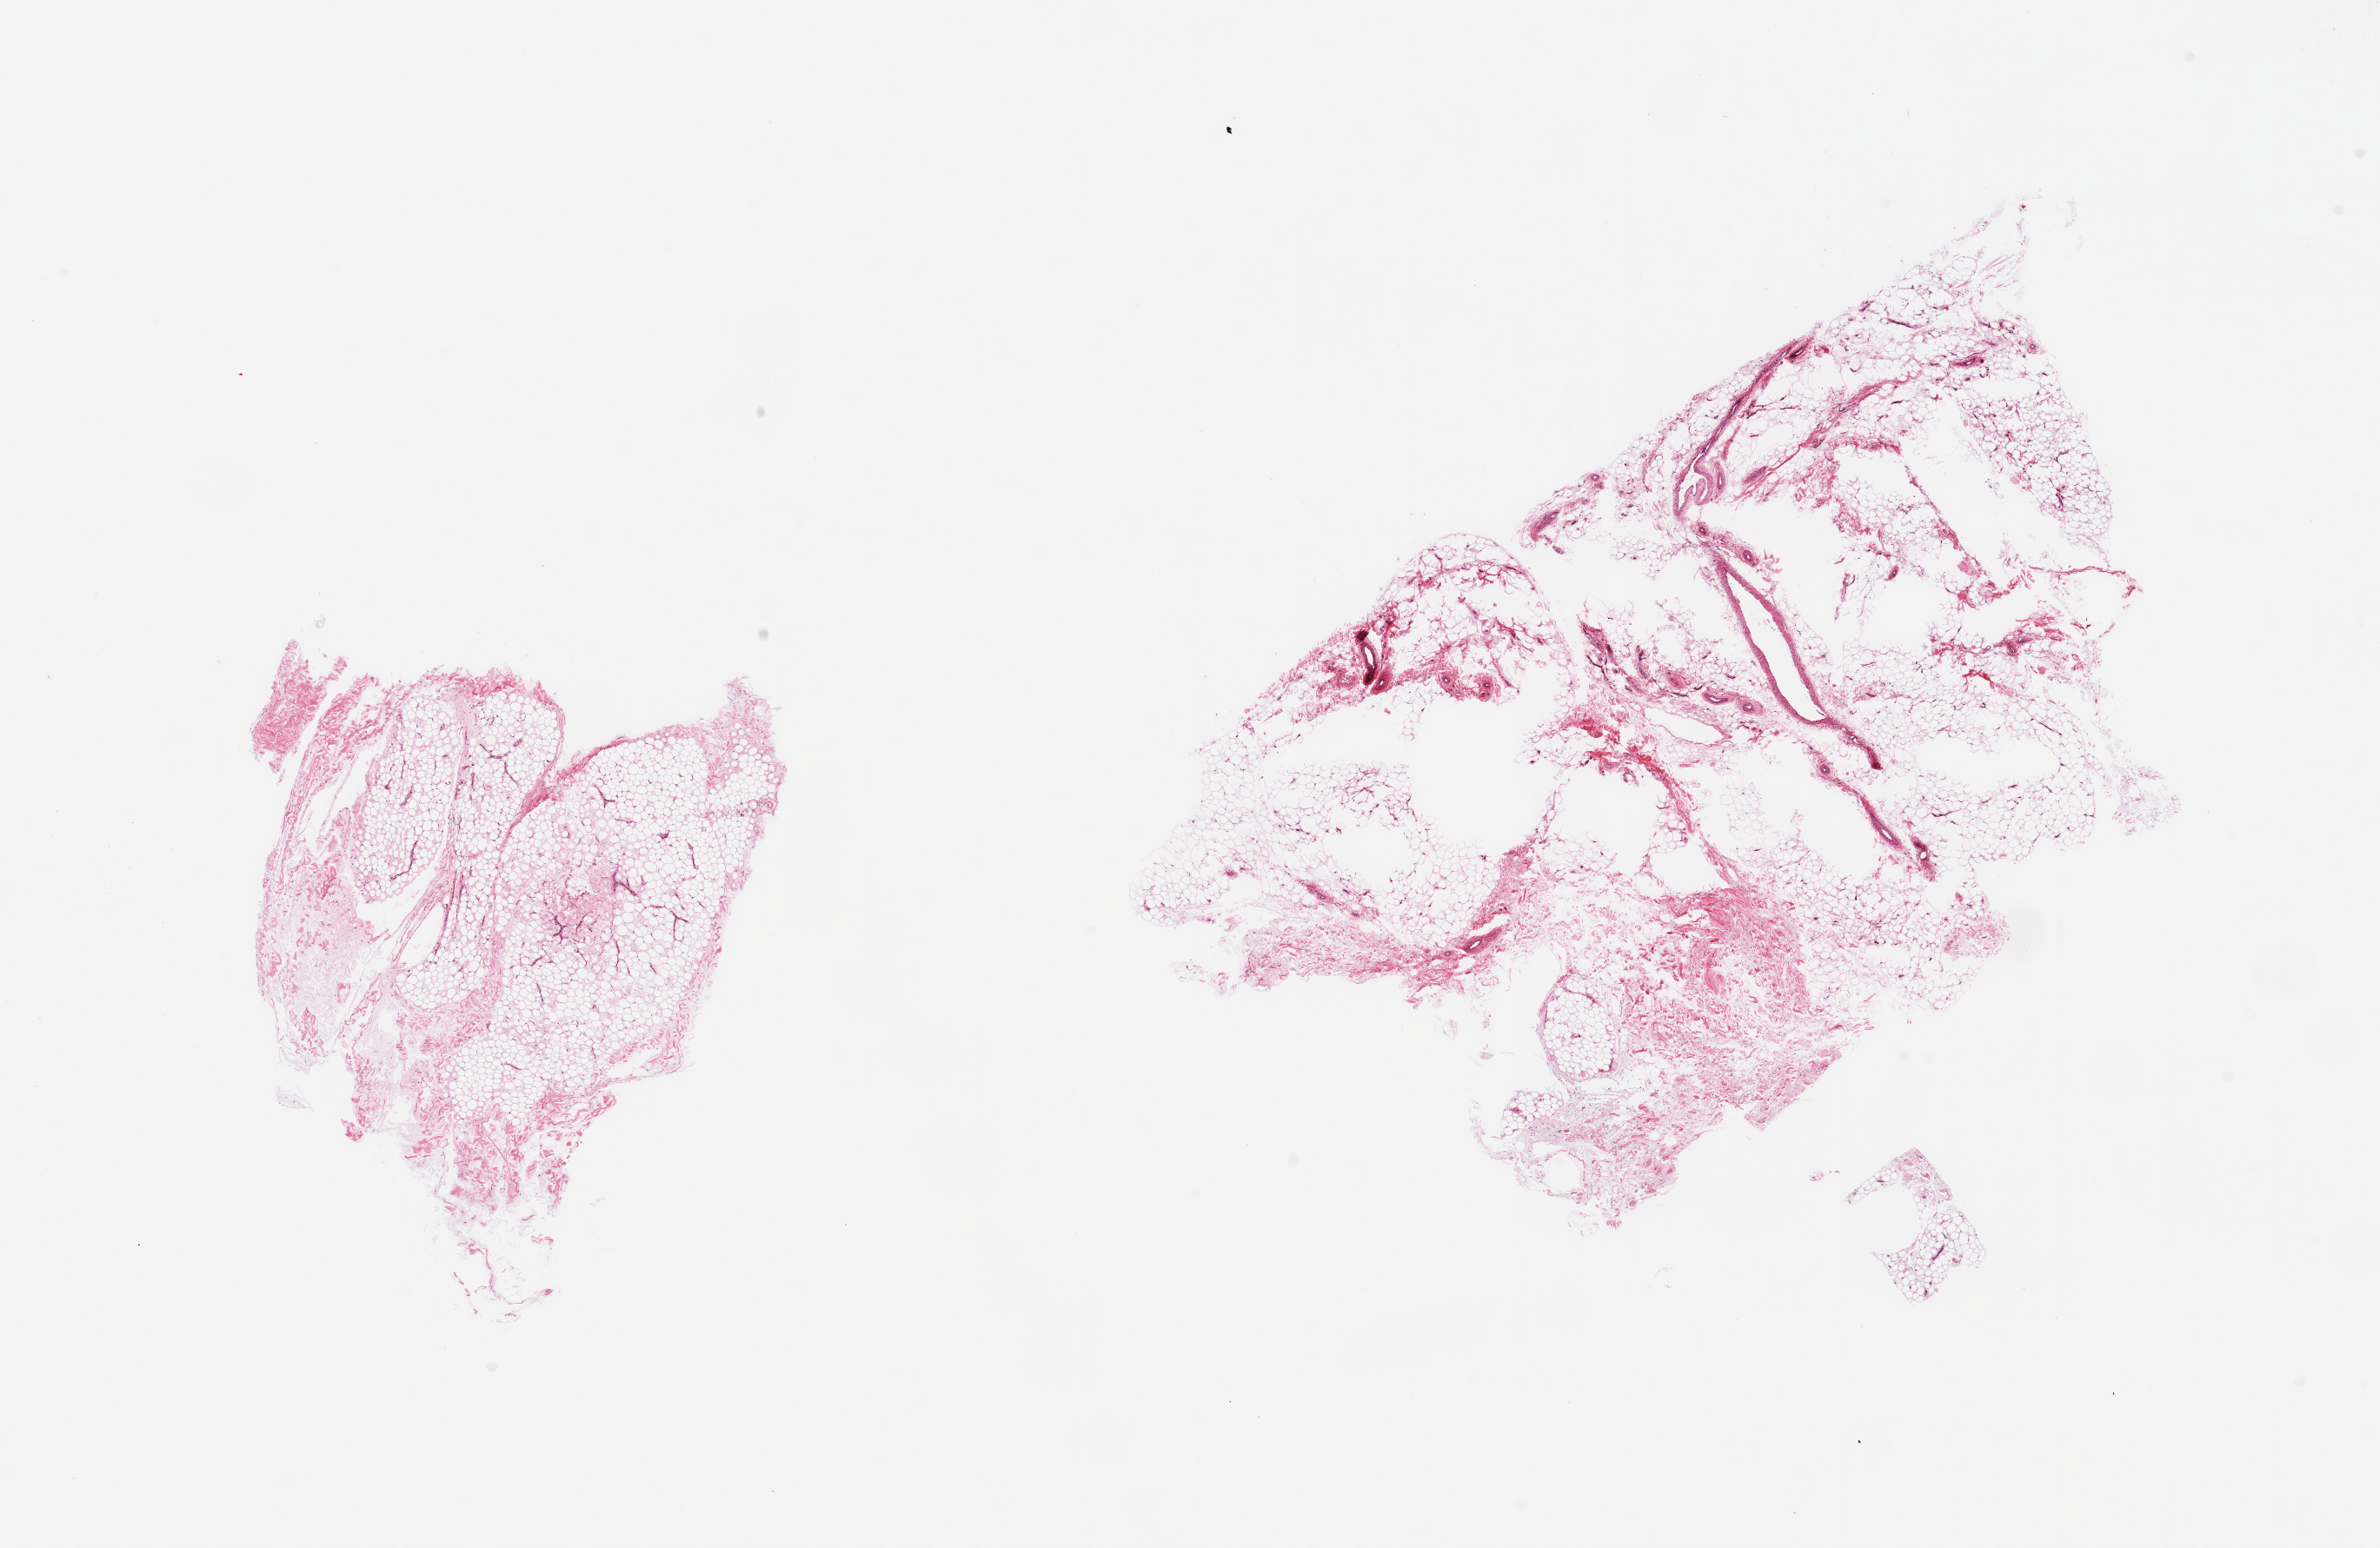
Whole-slide image, hematoxylin and eosin (H&E) stain — low-resolution overview of the scanned area, about 21.7 x 14.1 mm (slide scanned at 20x), PAXgene-fixed, paraffin-embedded tissue, section of adipose tissue (target tissue), tissue donor sample. Donor sex: male.
Review note (as recorded): 2 pieces; 10% vascular/fascia elements.